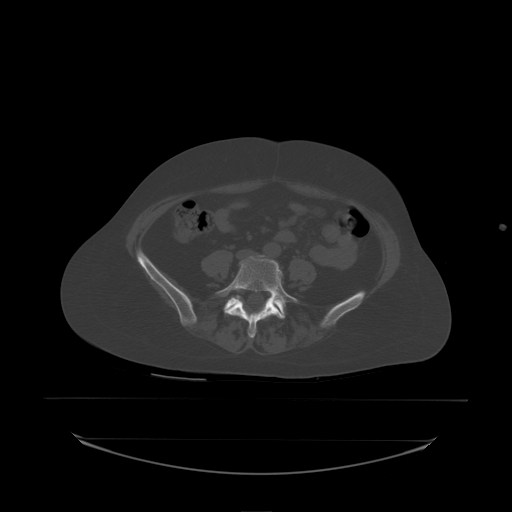
CT including the spine, one axial slice. Slice 39 of 242 in the series (ordered by position). Bone window (W 1800 / L 400 HU). 512 × 512 image matrix, field of view 500 × 500 mm. Female patient, age 53 years. Case-level facts recorded for this patient, not image findings: primary cancer: lung; vertebrae with lytic lesions (as recorded): T7, L1.
Structures marked on this image (semi-automatic segmentation, software-assisted and operator-edited):
- L5 vertebra: bounding box <216,255,298,338> (left, top, right, bottom; pixels)